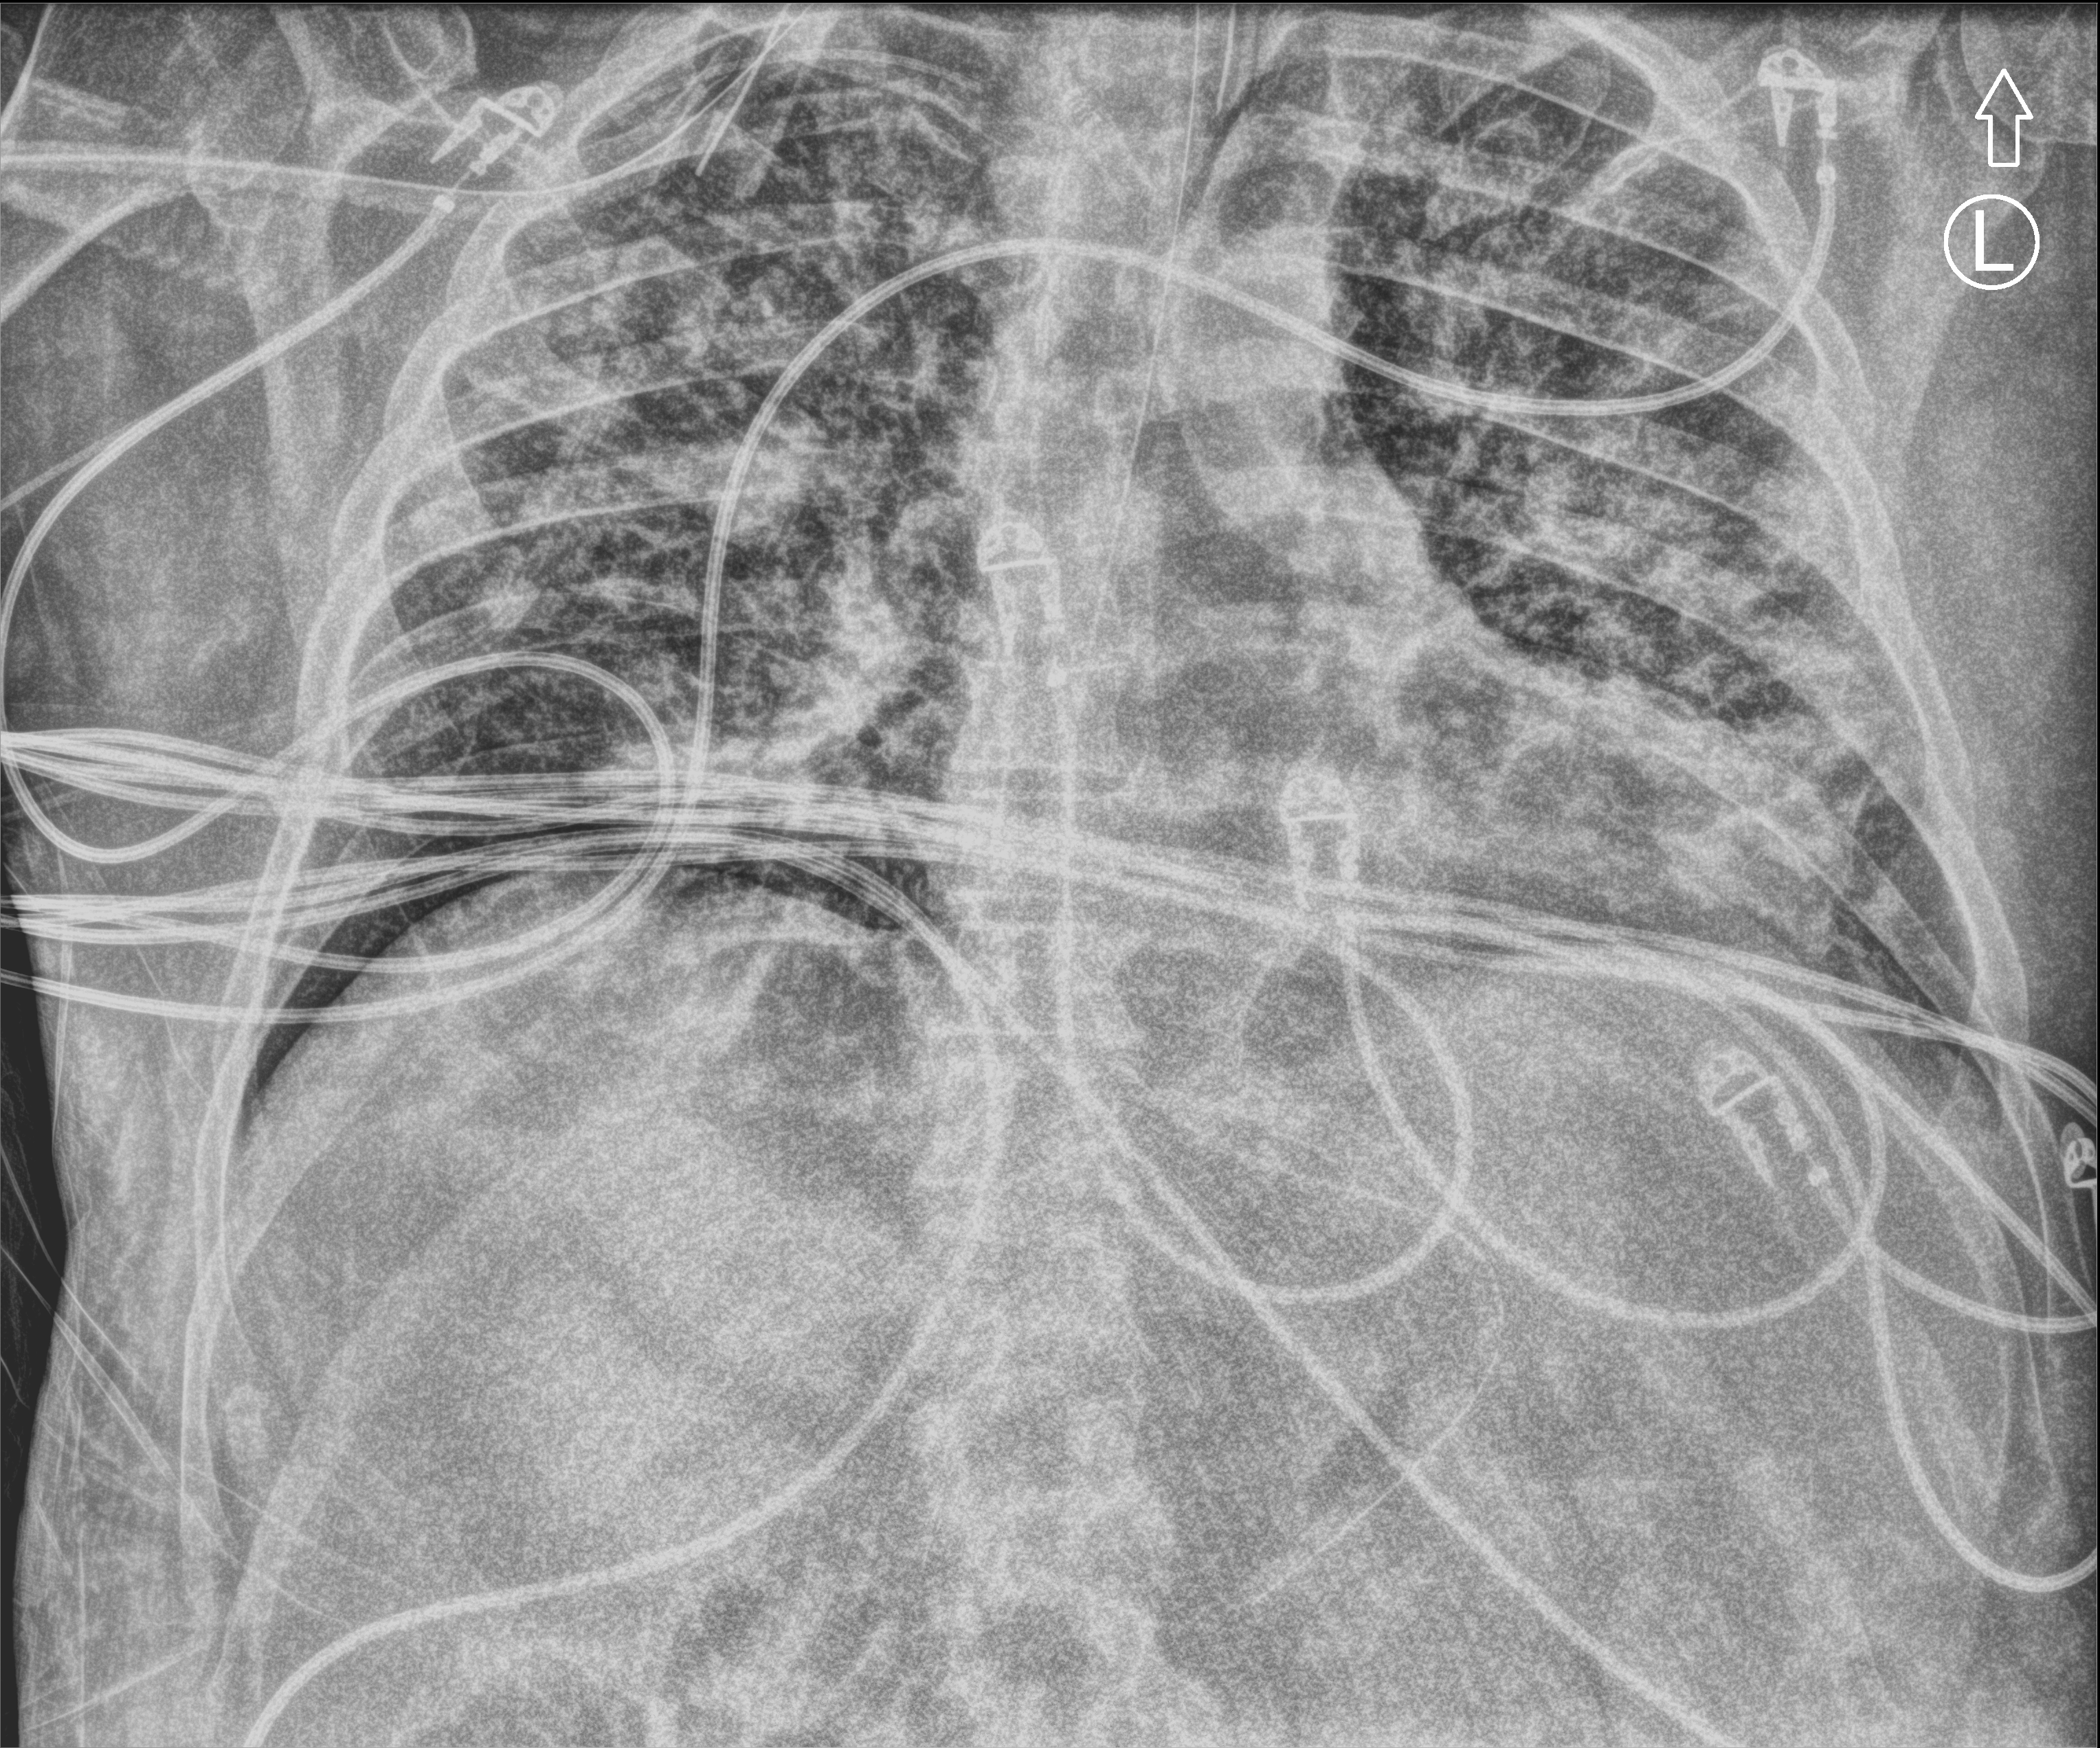
Chest X-ray (portable), anteroposterior (AP) projection. Patient hospitalised with COVID-19; male, aged 60–74 years.
Hospital-stay facts (about this admission, not read from this image; timing relative to this image not recorded):
- mechanically ventilated during this hospital stay: yes